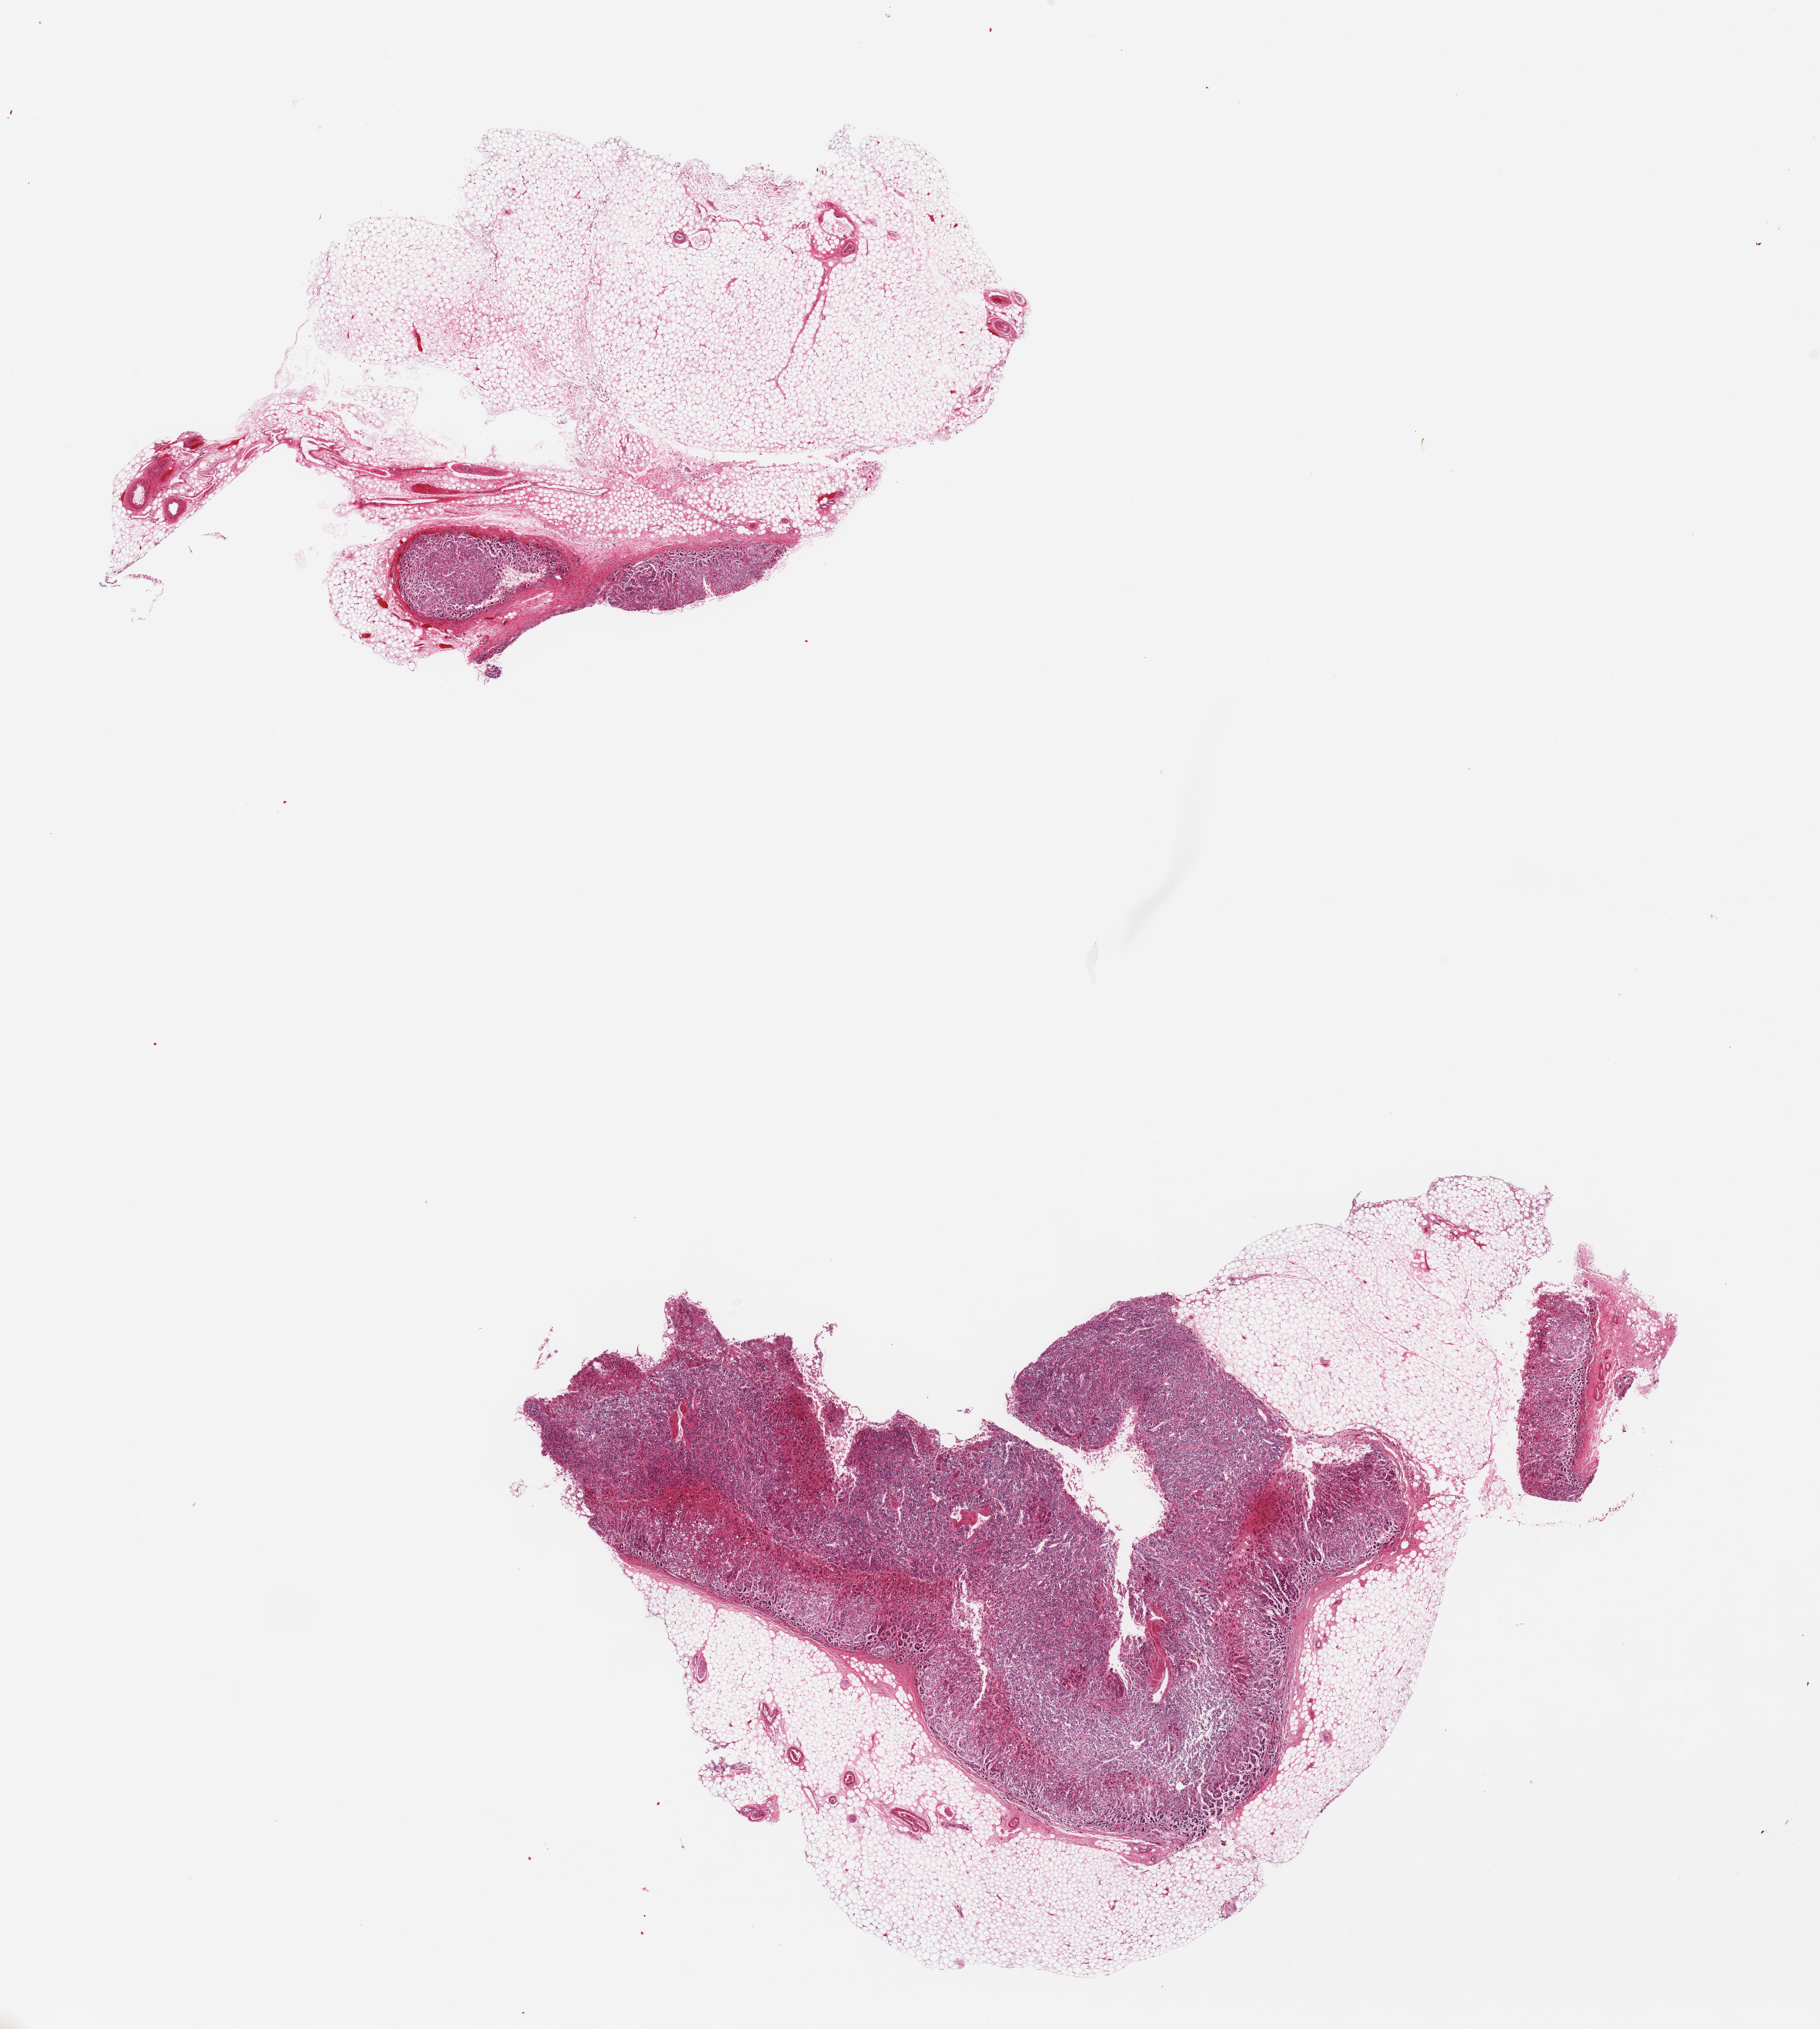
Hematoxylin and eosin (H&E) whole-slide image — low-resolution overview of the scanned area, about 18.7 x 20.9 mm (from a 20x scan); PAXgene-fixed paraffin-embedded (PFPE) section; section of adrenal gland (target tissue); tissue donor sample. Donor sex: female.
• pathologist's review note for this sample: 2 pieces; 1 has 80% external fat; other has 30% fat